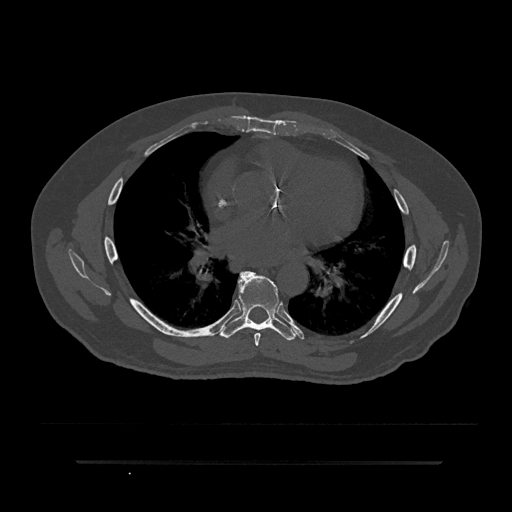
CT including the spine, one axial slice; position 494 of 797 along the scan axis; reconstruction kernel Br40s/3; 120 kVp; bone window (W 1800 / L 400 HU); 0.5 mm slice thickness; 512 × 512 image matrix, field of view 464 × 464 mm. Patient: male, 59 years. Case-level facts recorded for this patient, not image findings: primary cancer: bile ducts.
Structures marked on this image (semi-automatic segmentation, software-assisted and operator-edited):
- T6 vertebra: bounding box [x1, y1, x2, y2] px = [239, 275, 261, 346]
- T7 vertebra: [220, 271, 296, 341]